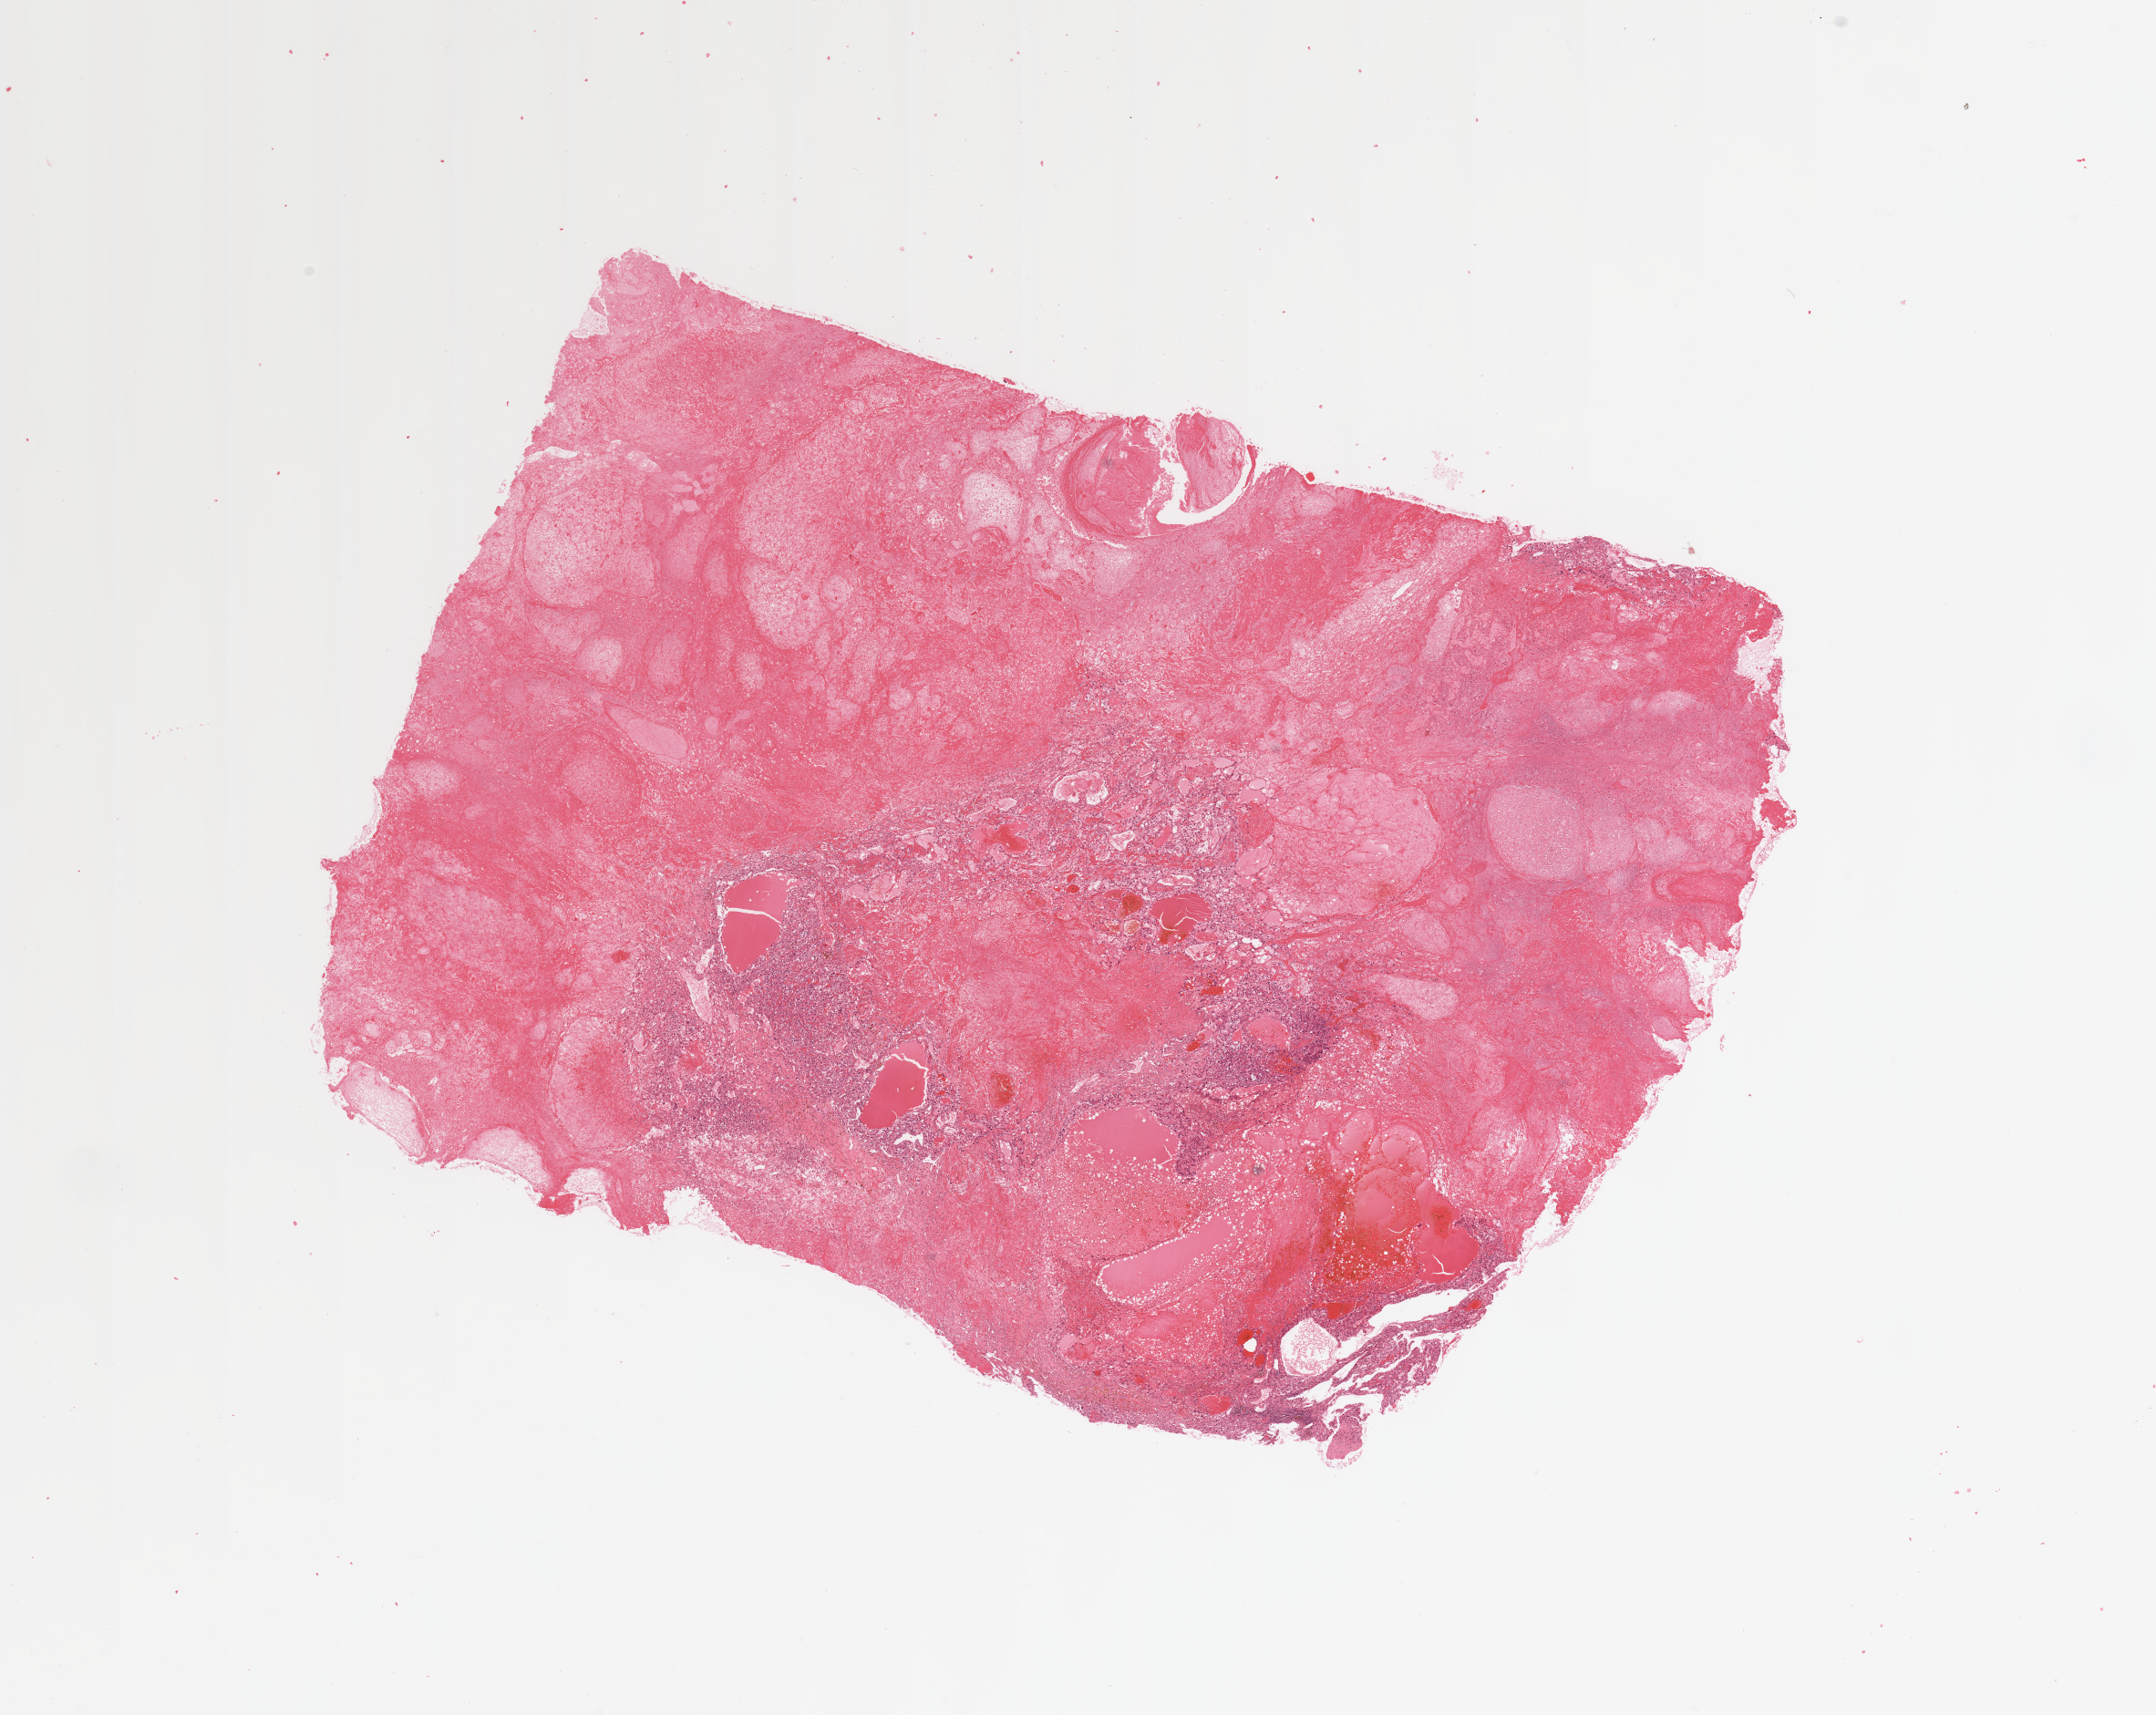
H&E-stained whole-slide image, a low-resolution overview of the entire scanned area, about 18.7 x 14.9 mm, tumour tissue sample, sampled site: kidney. Male, 72 y/o. Pathologist review of this section (percent, as recorded): tumour nuclei 60%, necrosis 70%.
Histologic diagnosis: Renal cell carcinoma, NOS.